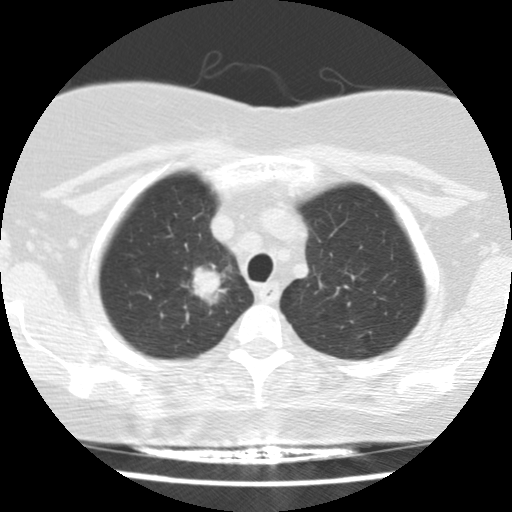
Axial slice from a low-dose chest CT screening exam; baseline annual screen; lung window (W 1500 / L -600 HU); standard (soft-tissue) reconstruction kernel (STANDARD); slice 23 of 148 in the series. Female, age 58 years at enrolment.
• Lesion marked by an expert reader, bounding box [x1, y1, x2, y2] px = [169, 243, 247, 321].
• Screening reader's record for this exam (one nodule recorded; not confirmed to be the boxed lesion): non-calcified nodule or mass ≥4 mm, right upper lobe, 28 × 24 mm, spiculated (stellate) margins, soft tissue attenuation.
• Official screen result: positive, change unspecified: nodule(s) >= 4 mm or enlarging nodule(s), mass(es), or other non-specific abnormalities suspicious for lung cancer.